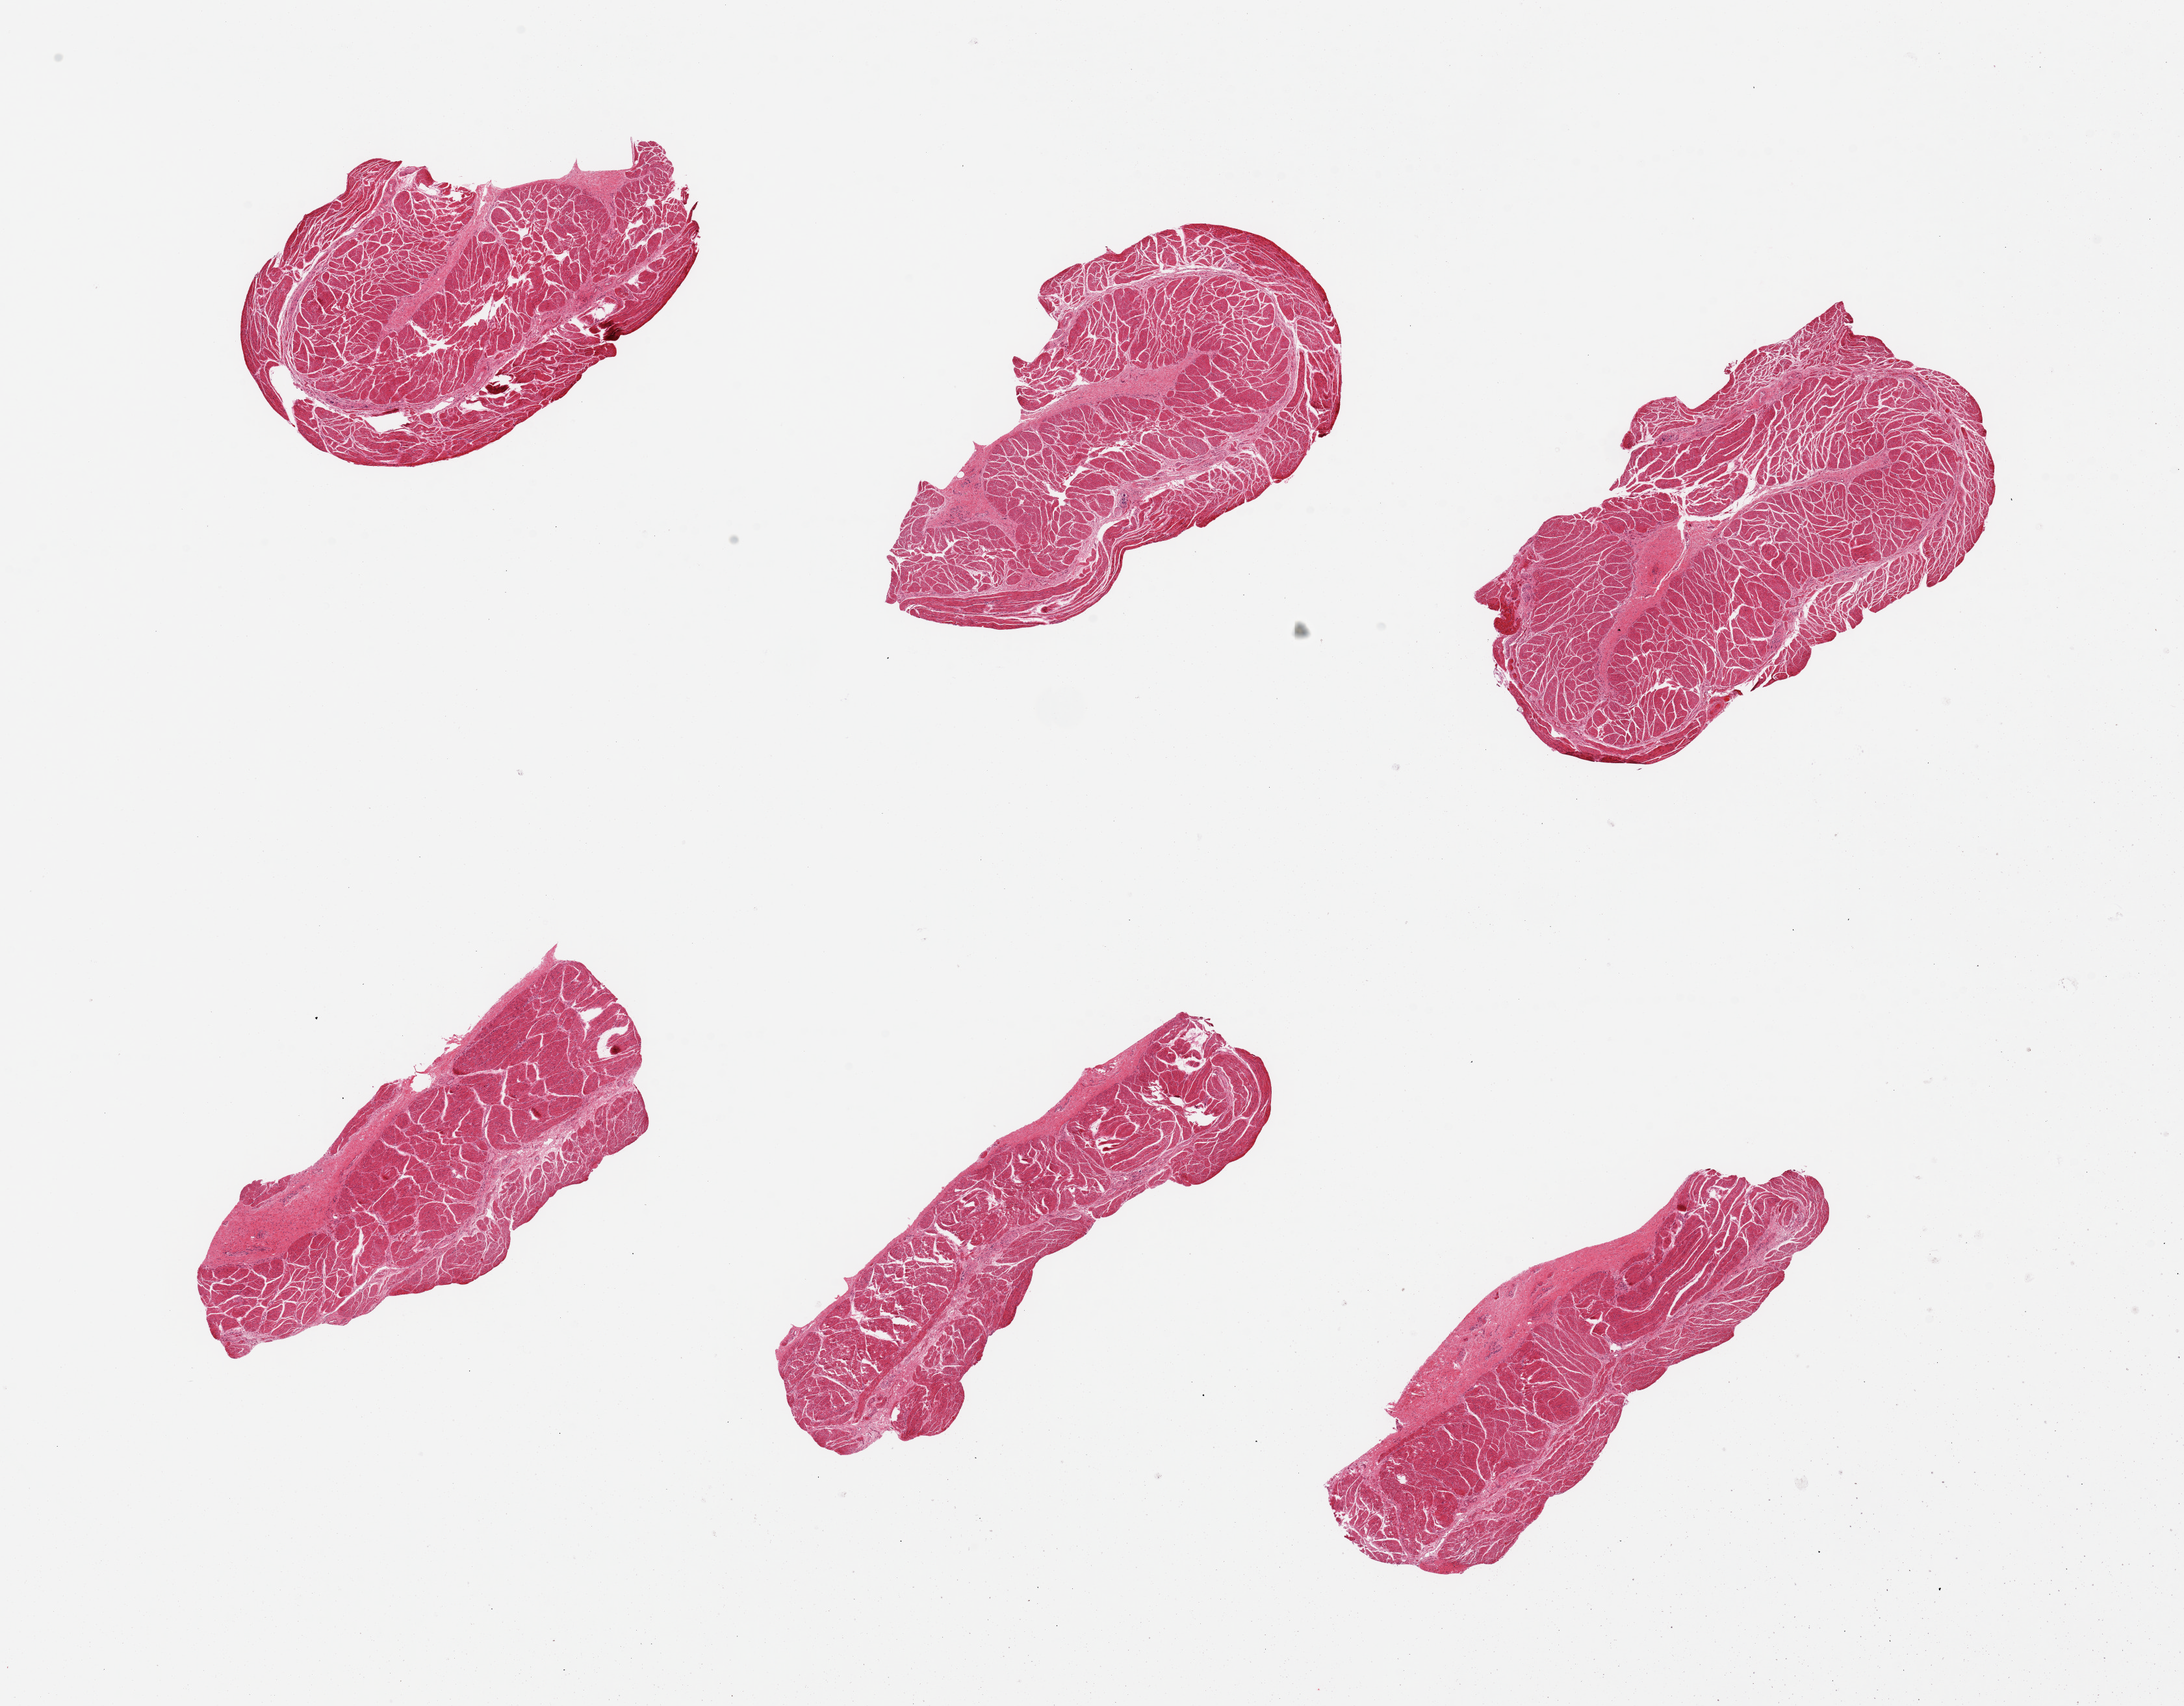
Digitized hematoxylin and eosin (H&E)-stained section, brightfield — shown as a low-resolution overview of the whole scanned area (about 26.6 x 20.8 mm, from a 20x scan), PAXgene-fixed paraffin-embedded (PFPE) section, sampled site (target tissue): esophageal muscle, donor tissue sample.
Reviewer comment on this tissue sample: 6 pieces, all muscularis, good specimens.